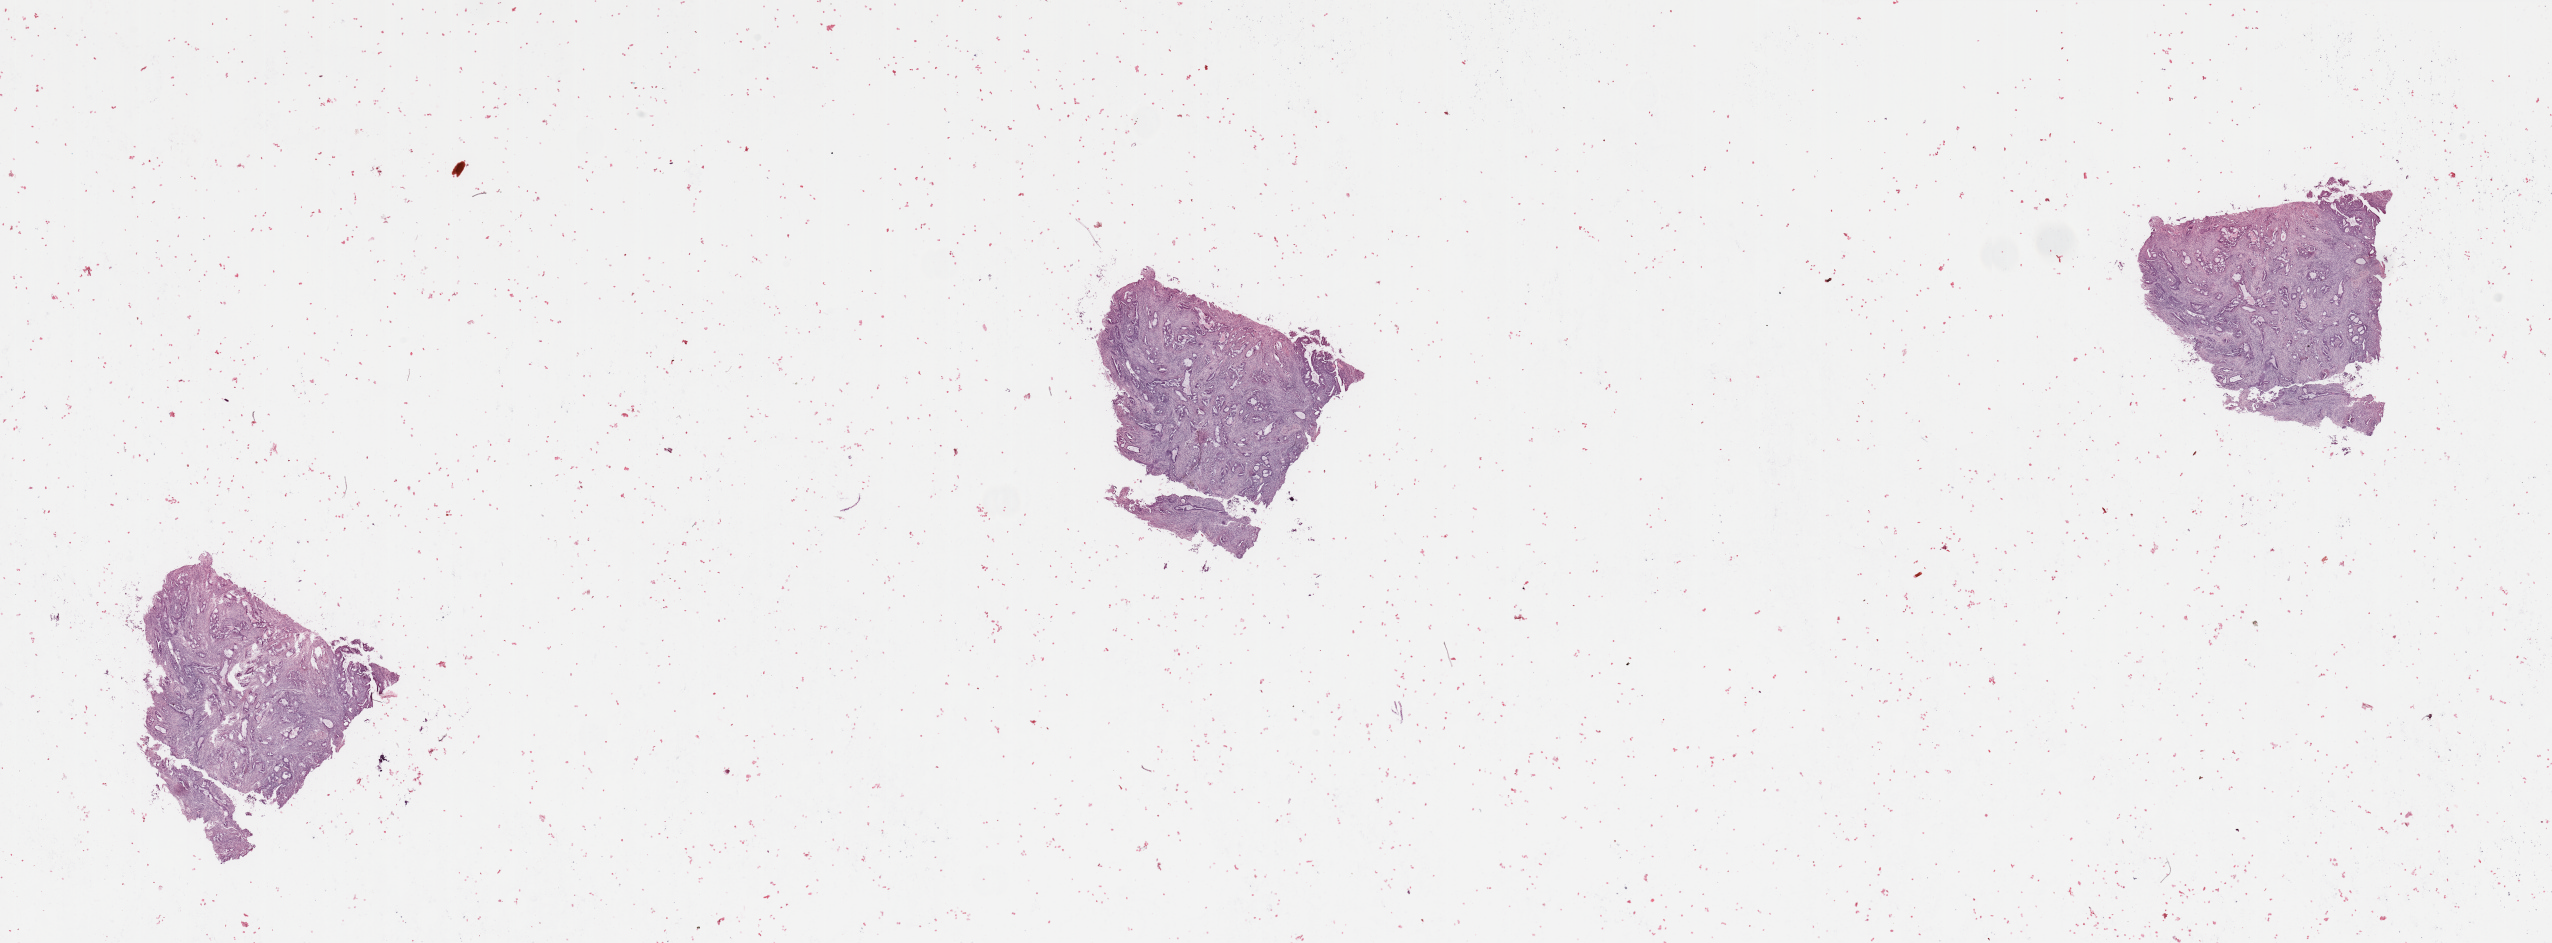
H&E-stained whole-slide image — a low-resolution overview of the entire scanned area, about 40.4 x 14.9 mm (acquisition: 20x scan); tumour tissue sample, sampled site: uterus. Patient: female, age 69 years. Histologic grade: G1 (well differentiated). Pathologist review of this section (percent, as recorded): tumour nuclei 80%, necrosis 2%.
Primary tumour site (as recorded): posterior endometrium. AJCC pathologic stage: II. Diagnosis: Endometrioid adenocarcinoma, NOS.